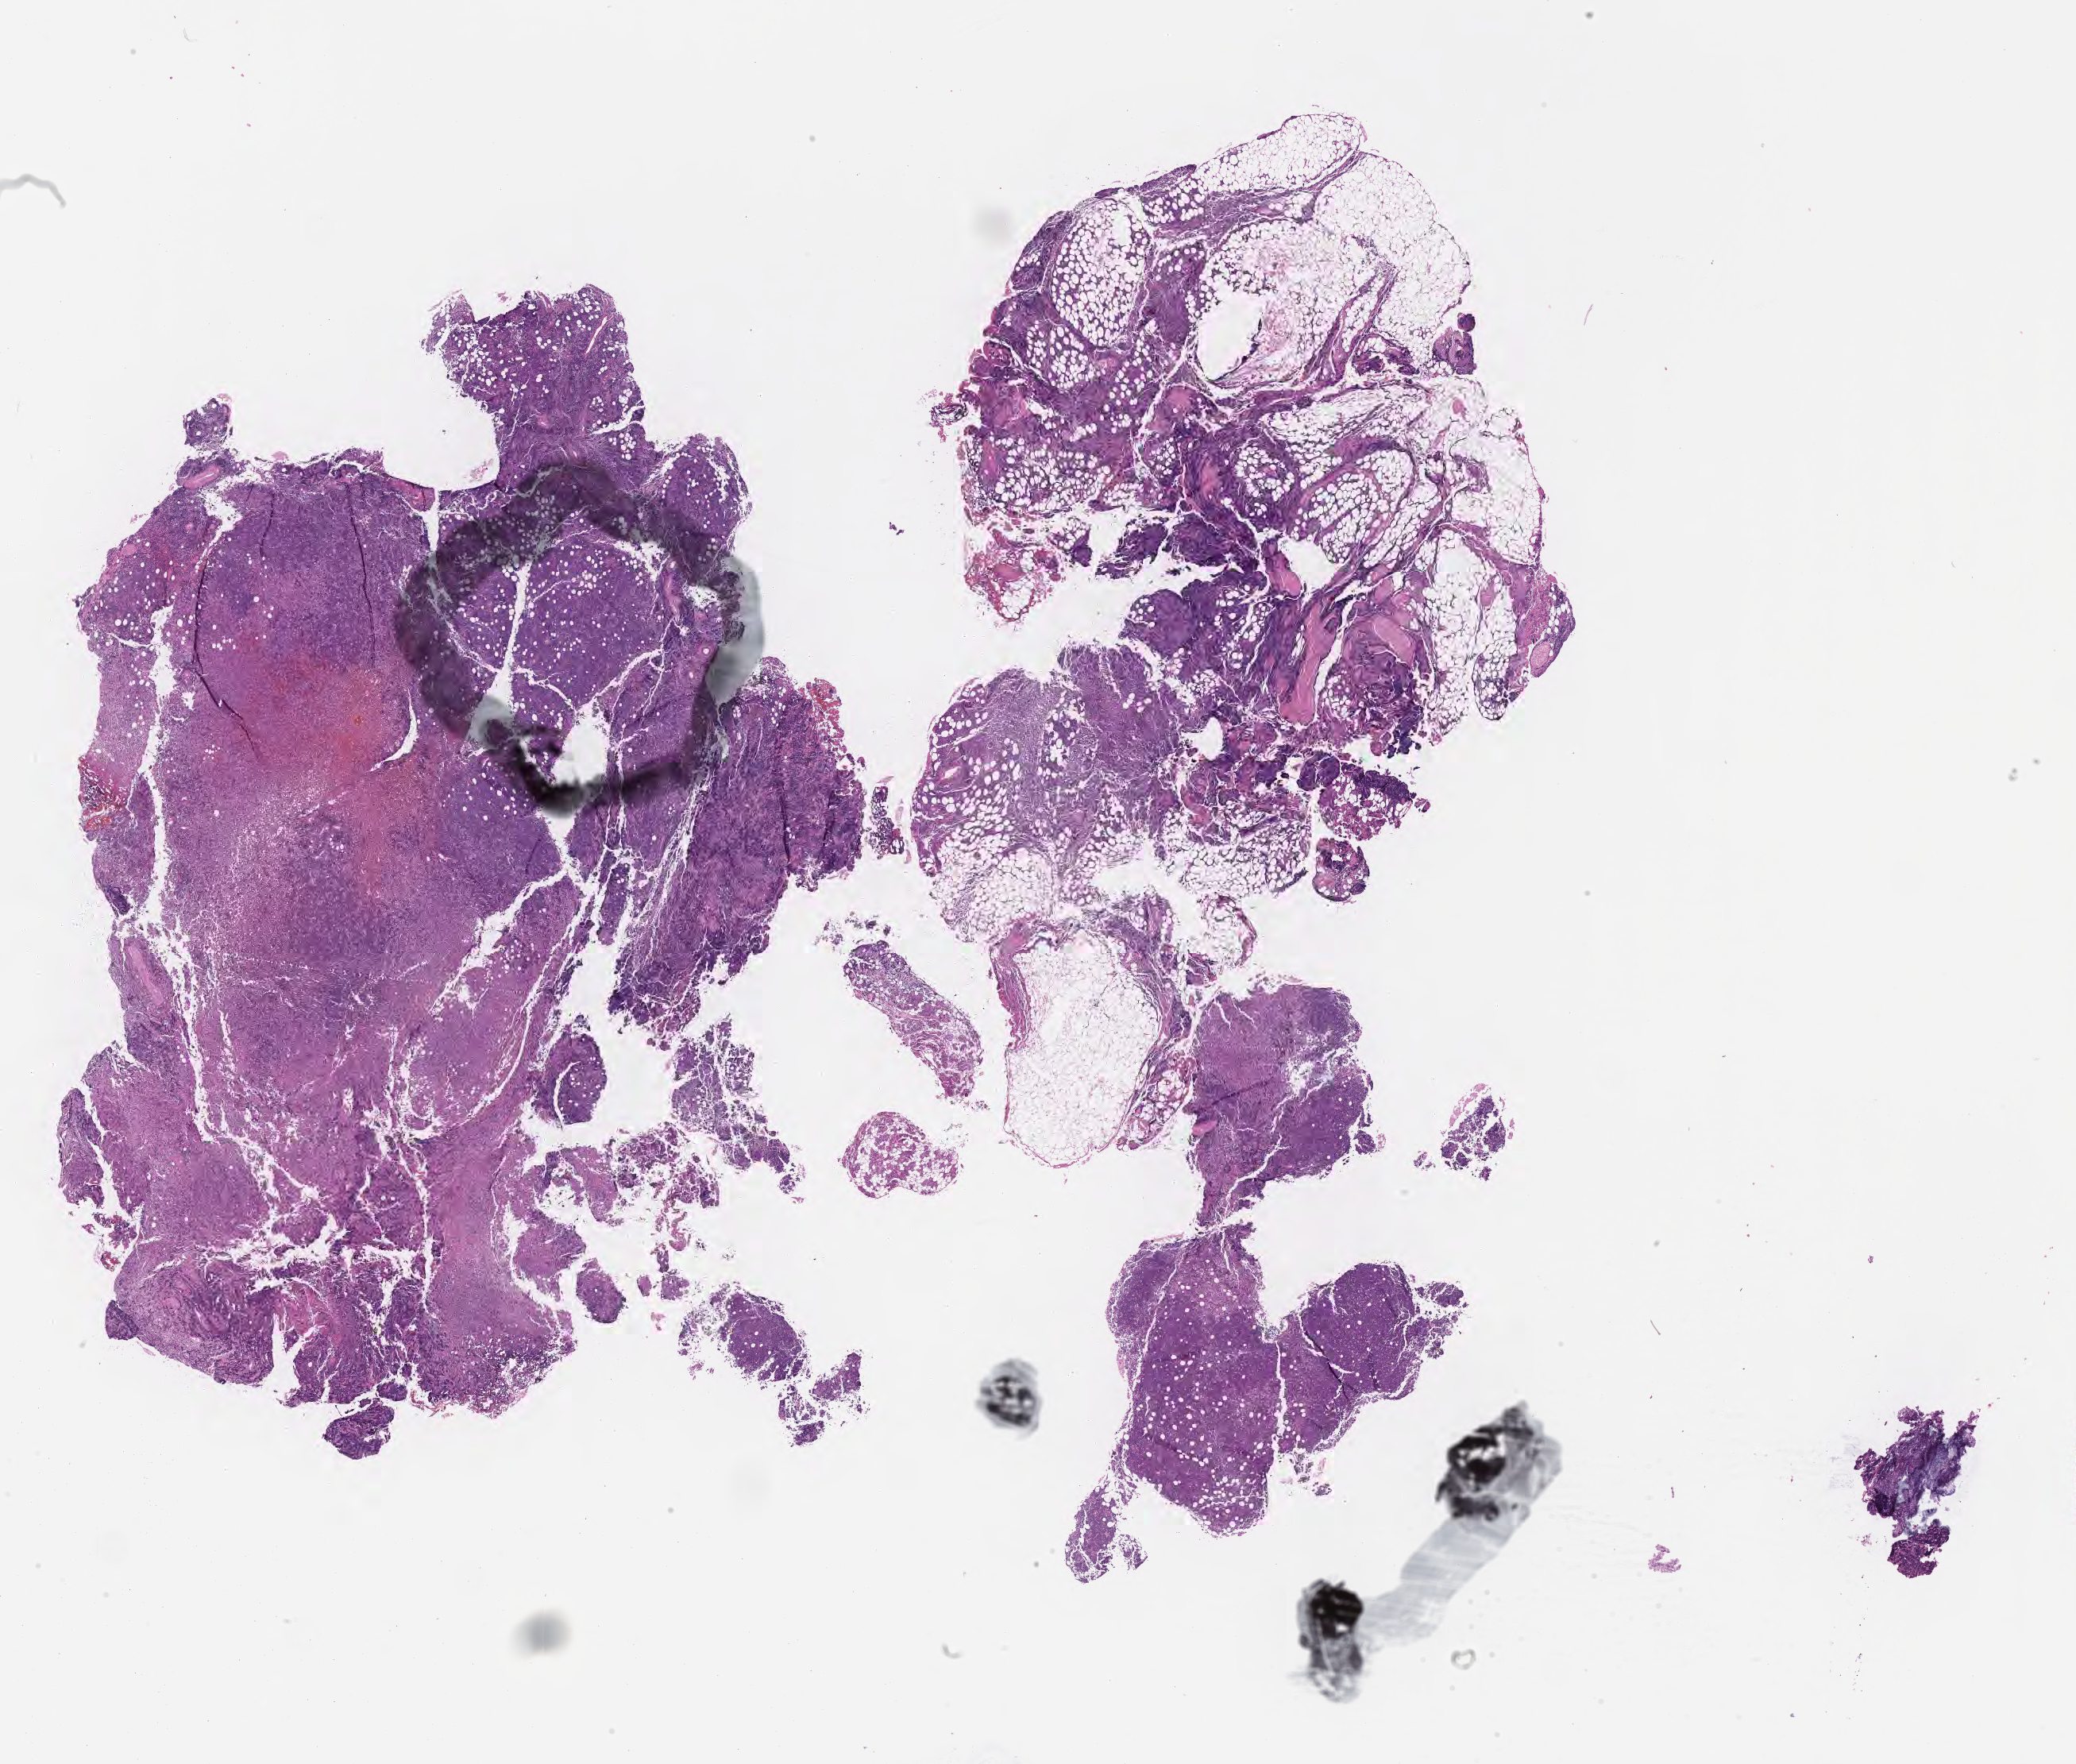
Whole-slide image, haematoxylin and eosin stain — shown as a low-resolution overview of the whole scanned area (about 21.1 x 18.0 mm), specimen: tumor tissue. Female patient, age 70 years.
- diagnosis: Burkitt lymphoma, NOS